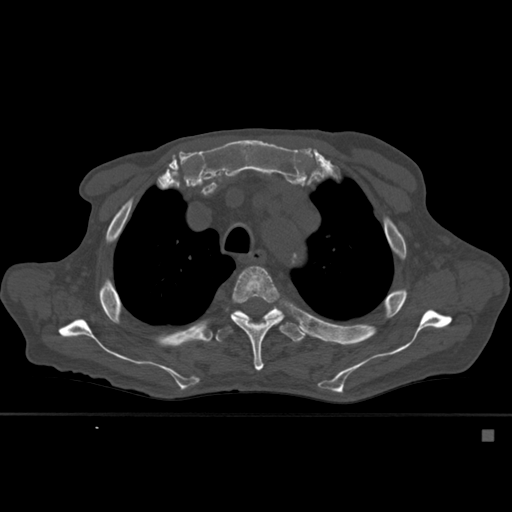
CT including the spine, one axial slice; slice 413 of 527 in the series (ordered by position); bone window (W 1800 / L 400 HU); 1.5 mm slice thickness; 512 × 512 image matrix, field of view 373 × 373 mm. Patient: male, 78 years. From the clinical record (not read from this slice): primary cancer: prostate.
Annotated regions visible in this slice (semi-automatically segmented with operator editing):
- T4 vertebra: bounding box (x1, y1, x2, y2) in pixels: (231, 266, 284, 371)
- T5 vertebra: (215, 307, 309, 343)